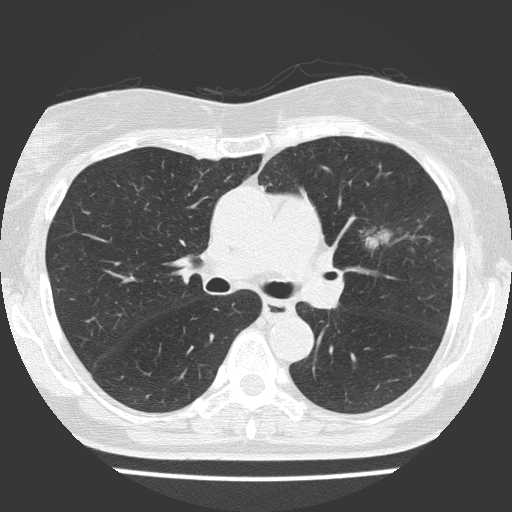
Axial slice from a low-dose chest CT screening exam, first (baseline) screen, lung window (W 1500 / L -600 HU), 120 kVp, 512 × 512 image matrix. Female participant, aged 70 years at enrolment.
Expert-annotated lung lesion, bounding box (x1, y1, x2, y2) in pixels: (328, 195, 433, 285). The screening reader recorded 2 non-calcified nodules or masses ≥4 mm on this exam (left upper lobe, right upper lobe); which of them this box marks is not recorded. Later outcome: lung cancer diagnosed 25 days after this screen — adenocarcinoma, NOS, left upper lobe, poorly differentiated (G3), stage IV (AJCC 6th edition), 30 mm at pathology.